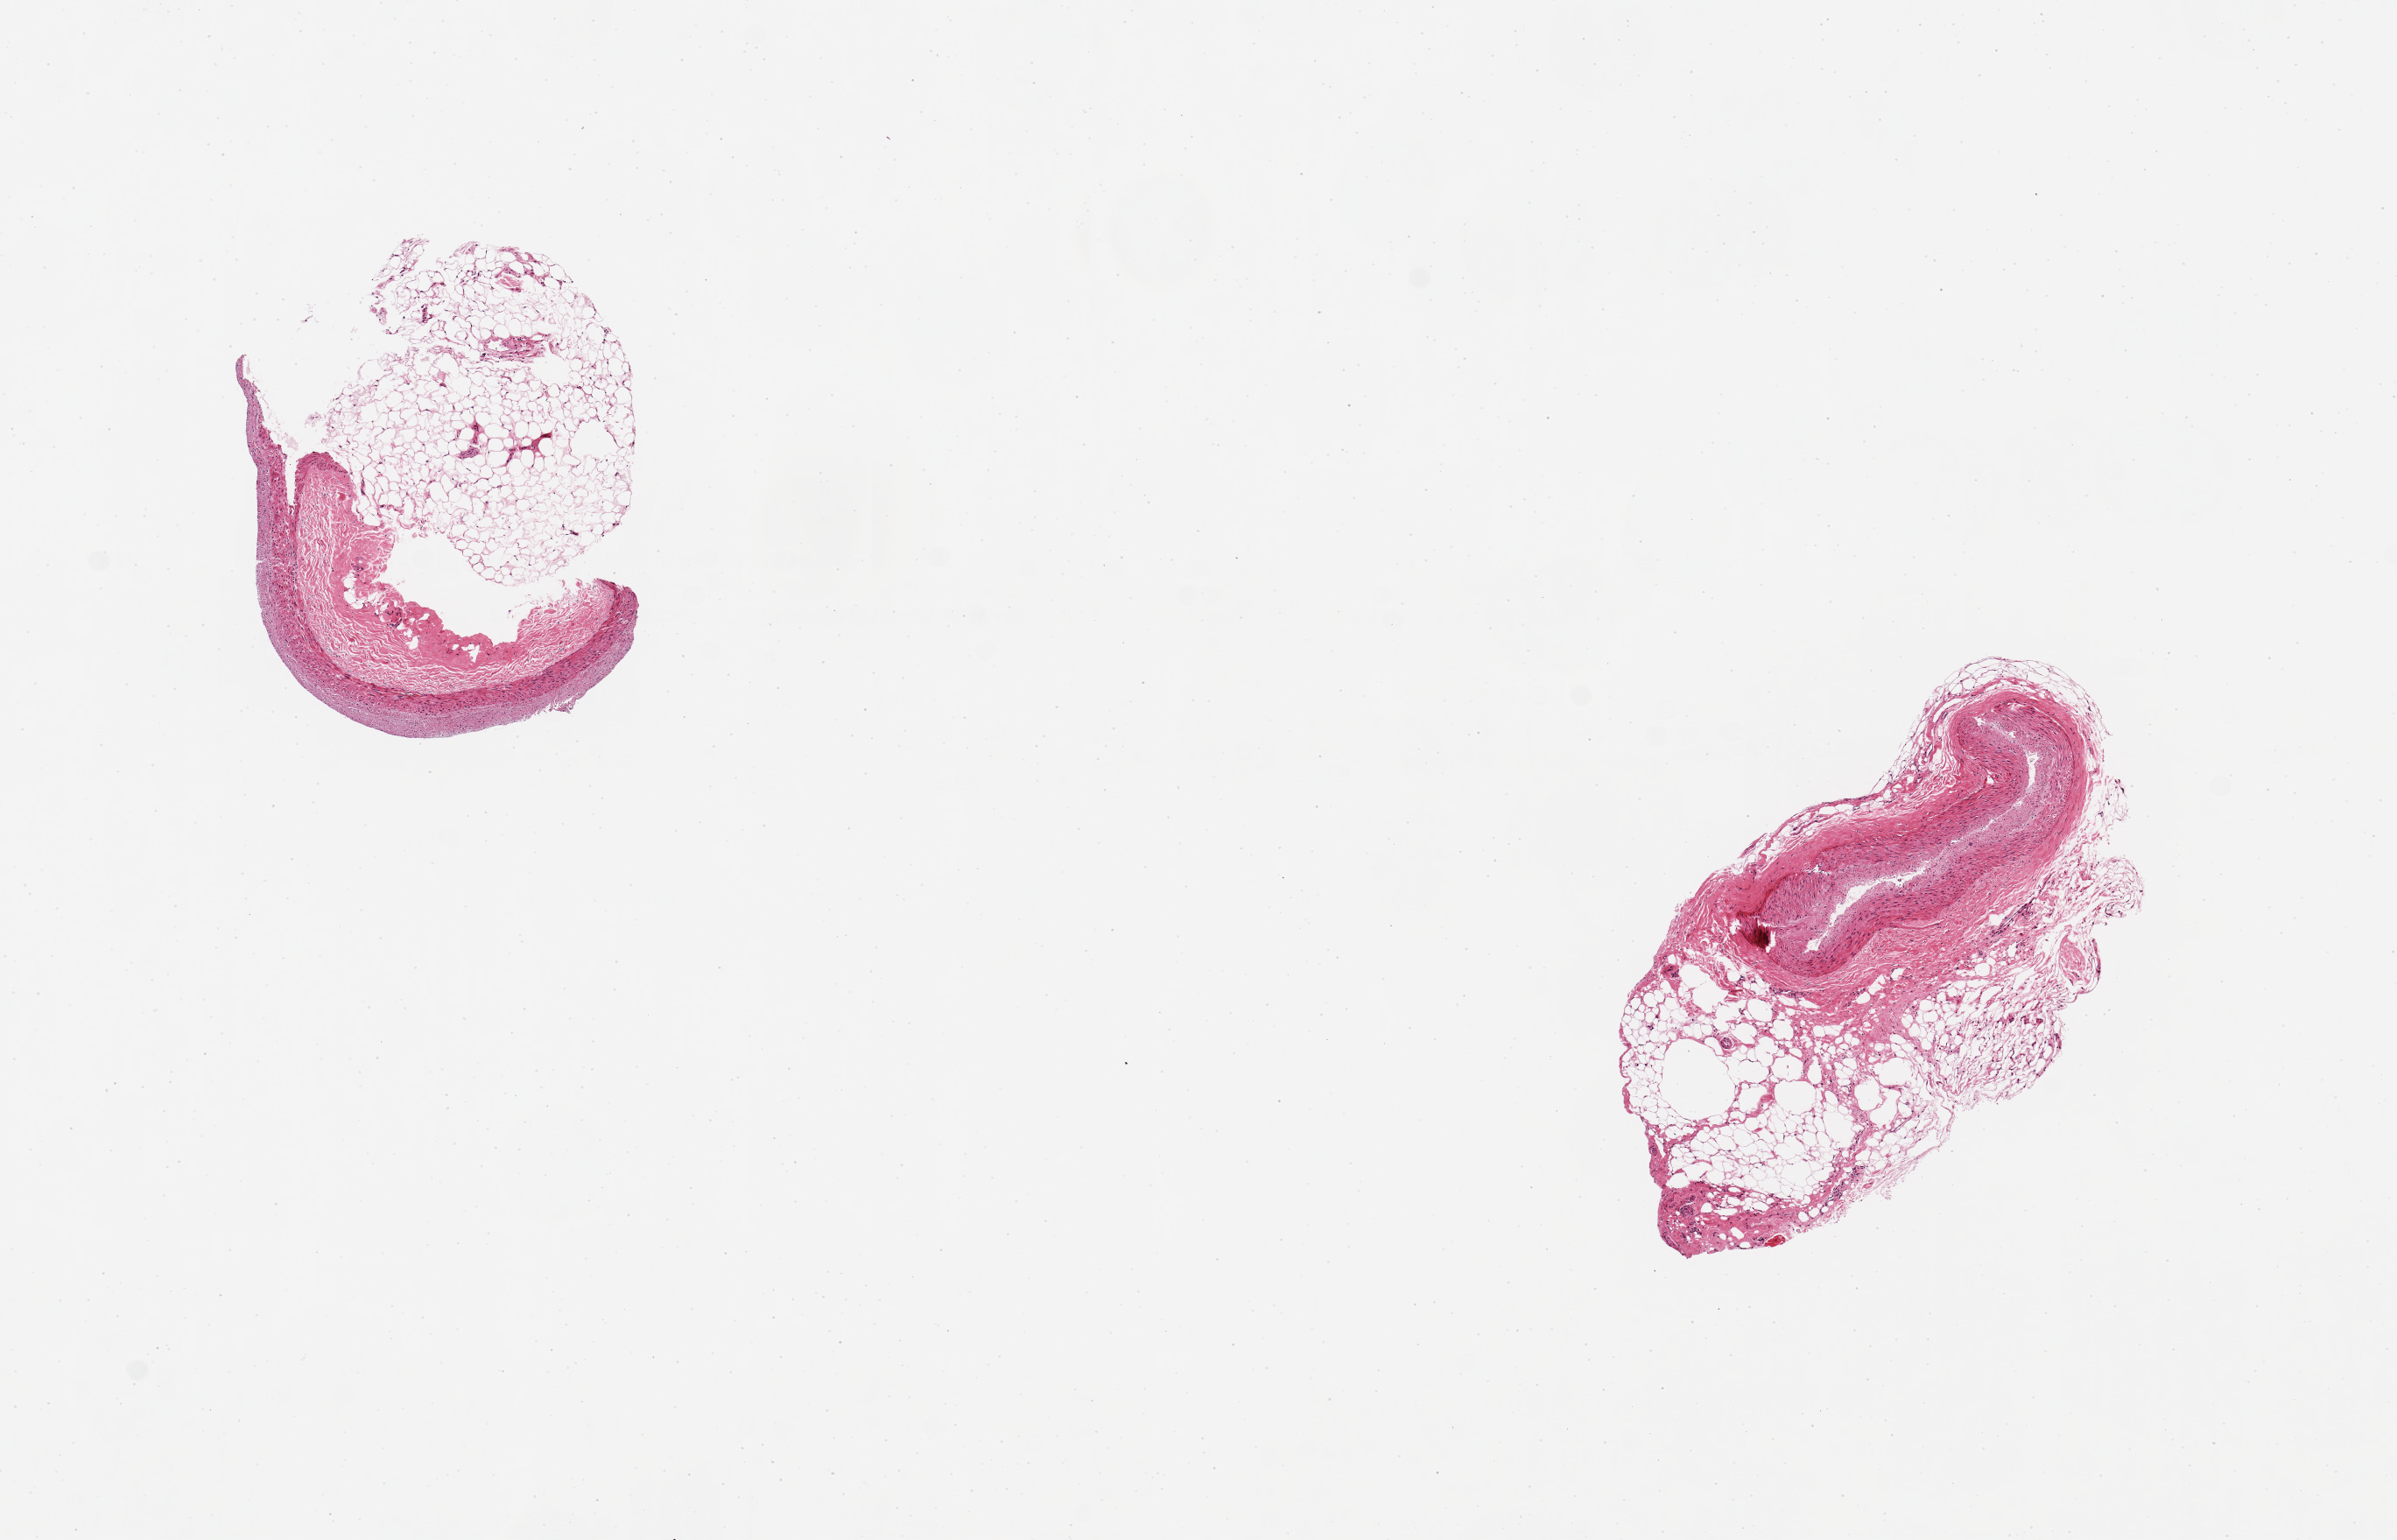
Hematoxylin and eosin (H&E) whole-slide image — shown as a low-resolution overview of the whole scanned area (about 10.8 x 7.0 mm). PAXgene-fixed paraffin-embedded (PFPE) section. Section of coronary artery (target tissue). Tissue donor sample. Donor: female.
Review note (as recorded): 2 pieces, 2x2 & 3x1.5 mm; >50% adipose.